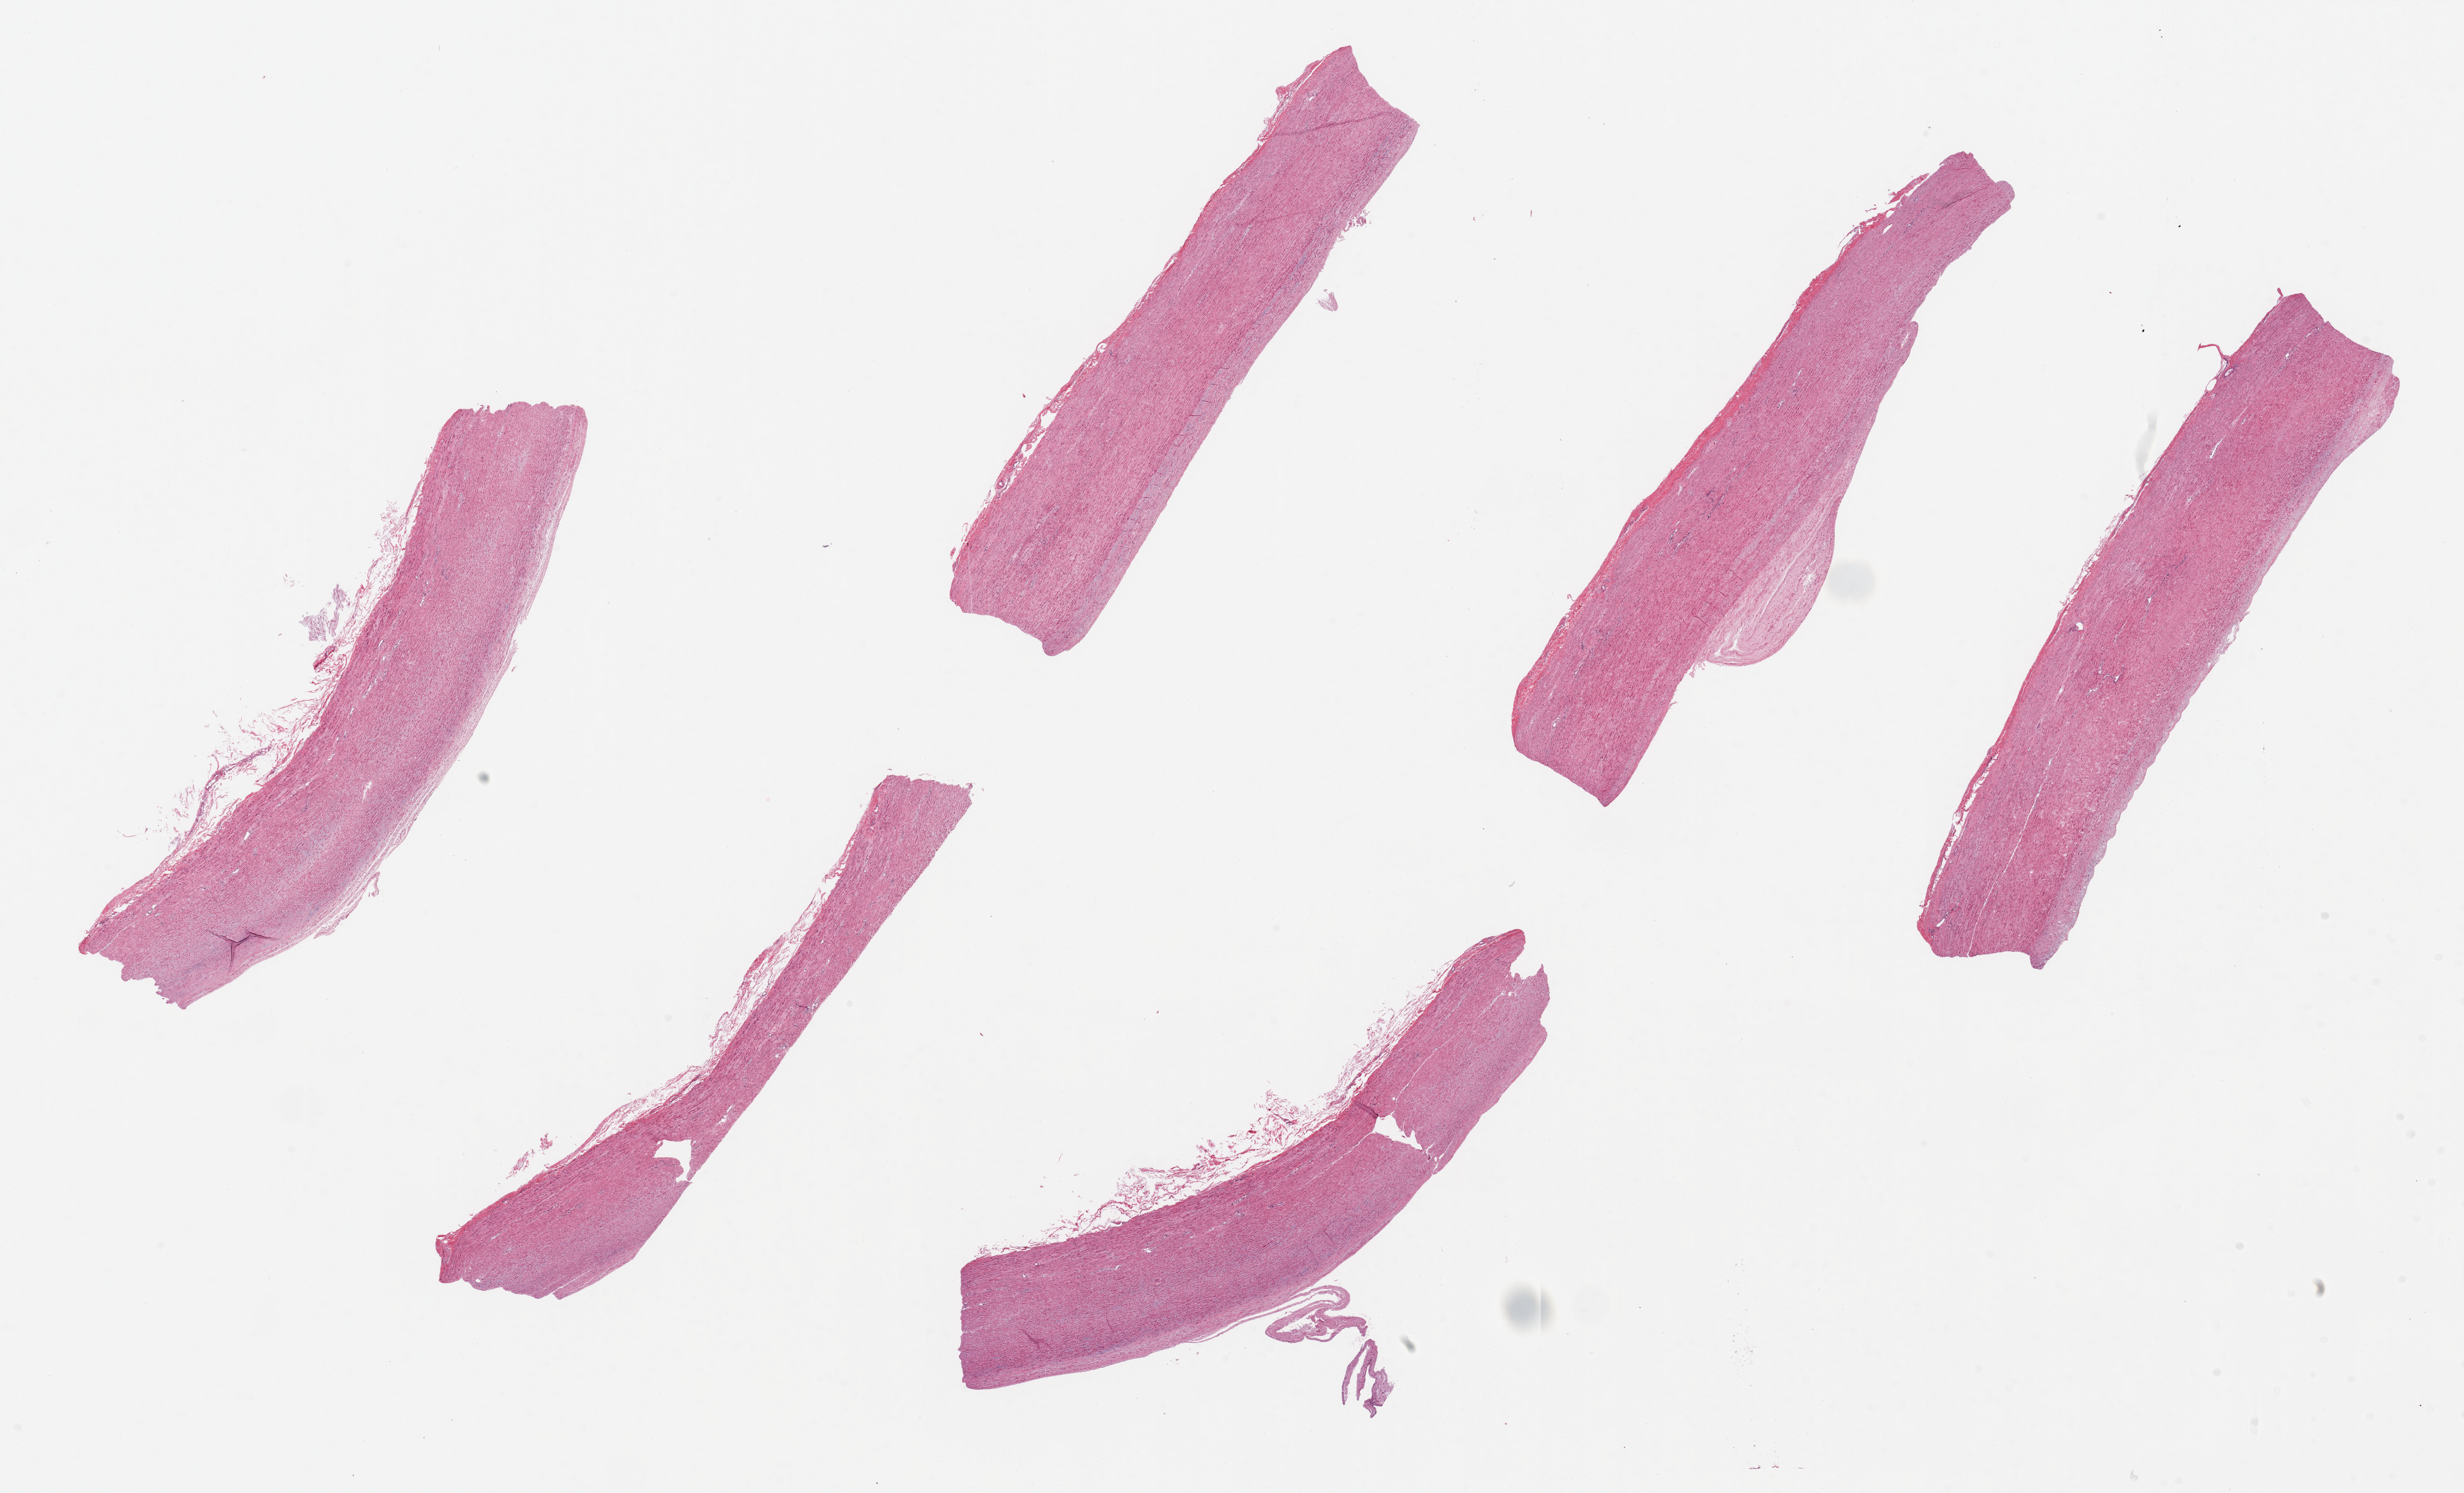
H&E whole-slide image, a low-resolution overview of the entire scanned area, about 31.5 x 19.1 mm (slide scanned at 20x). PAXgene-fixed, paraffin-embedded tissue. Sampled site (target tissue): aorta. Tissue donor sample. Donor: male.
- pathologist's review note for this sample: 6 pieces up to 9x4 mm; no adventitial adipose